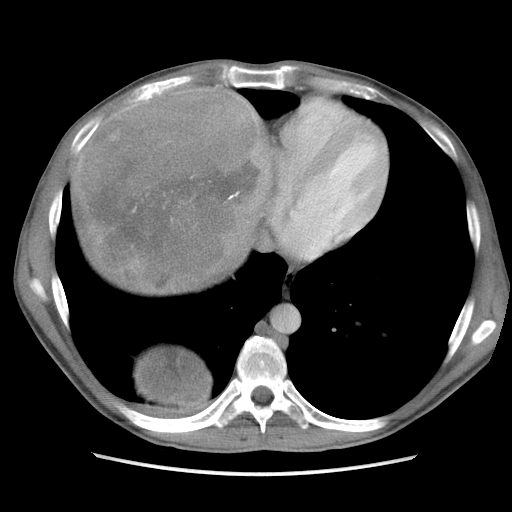
Contrast-enhanced abdominal CT, one axial slice; position 96 of 115 along the scan axis; soft-tissue window (W 400 / L 40 HU); 5 mm slice thickness; 512 × 512 image matrix, field of view 360 × 360 mm. Male patient. Case-level facts recorded for this patient, not image findings: diagnosis: adrenocortical carcinoma; tumour side: right adrenal; Ki-67 index: 13 %; stage (as recorded): 3.
Annotated regions visible in this slice (semi-automatic segmentation, software-assisted and operator-edited):
- mass: bounding box (x1, y1, x2, y2) in pixels: (74, 90, 266, 406)